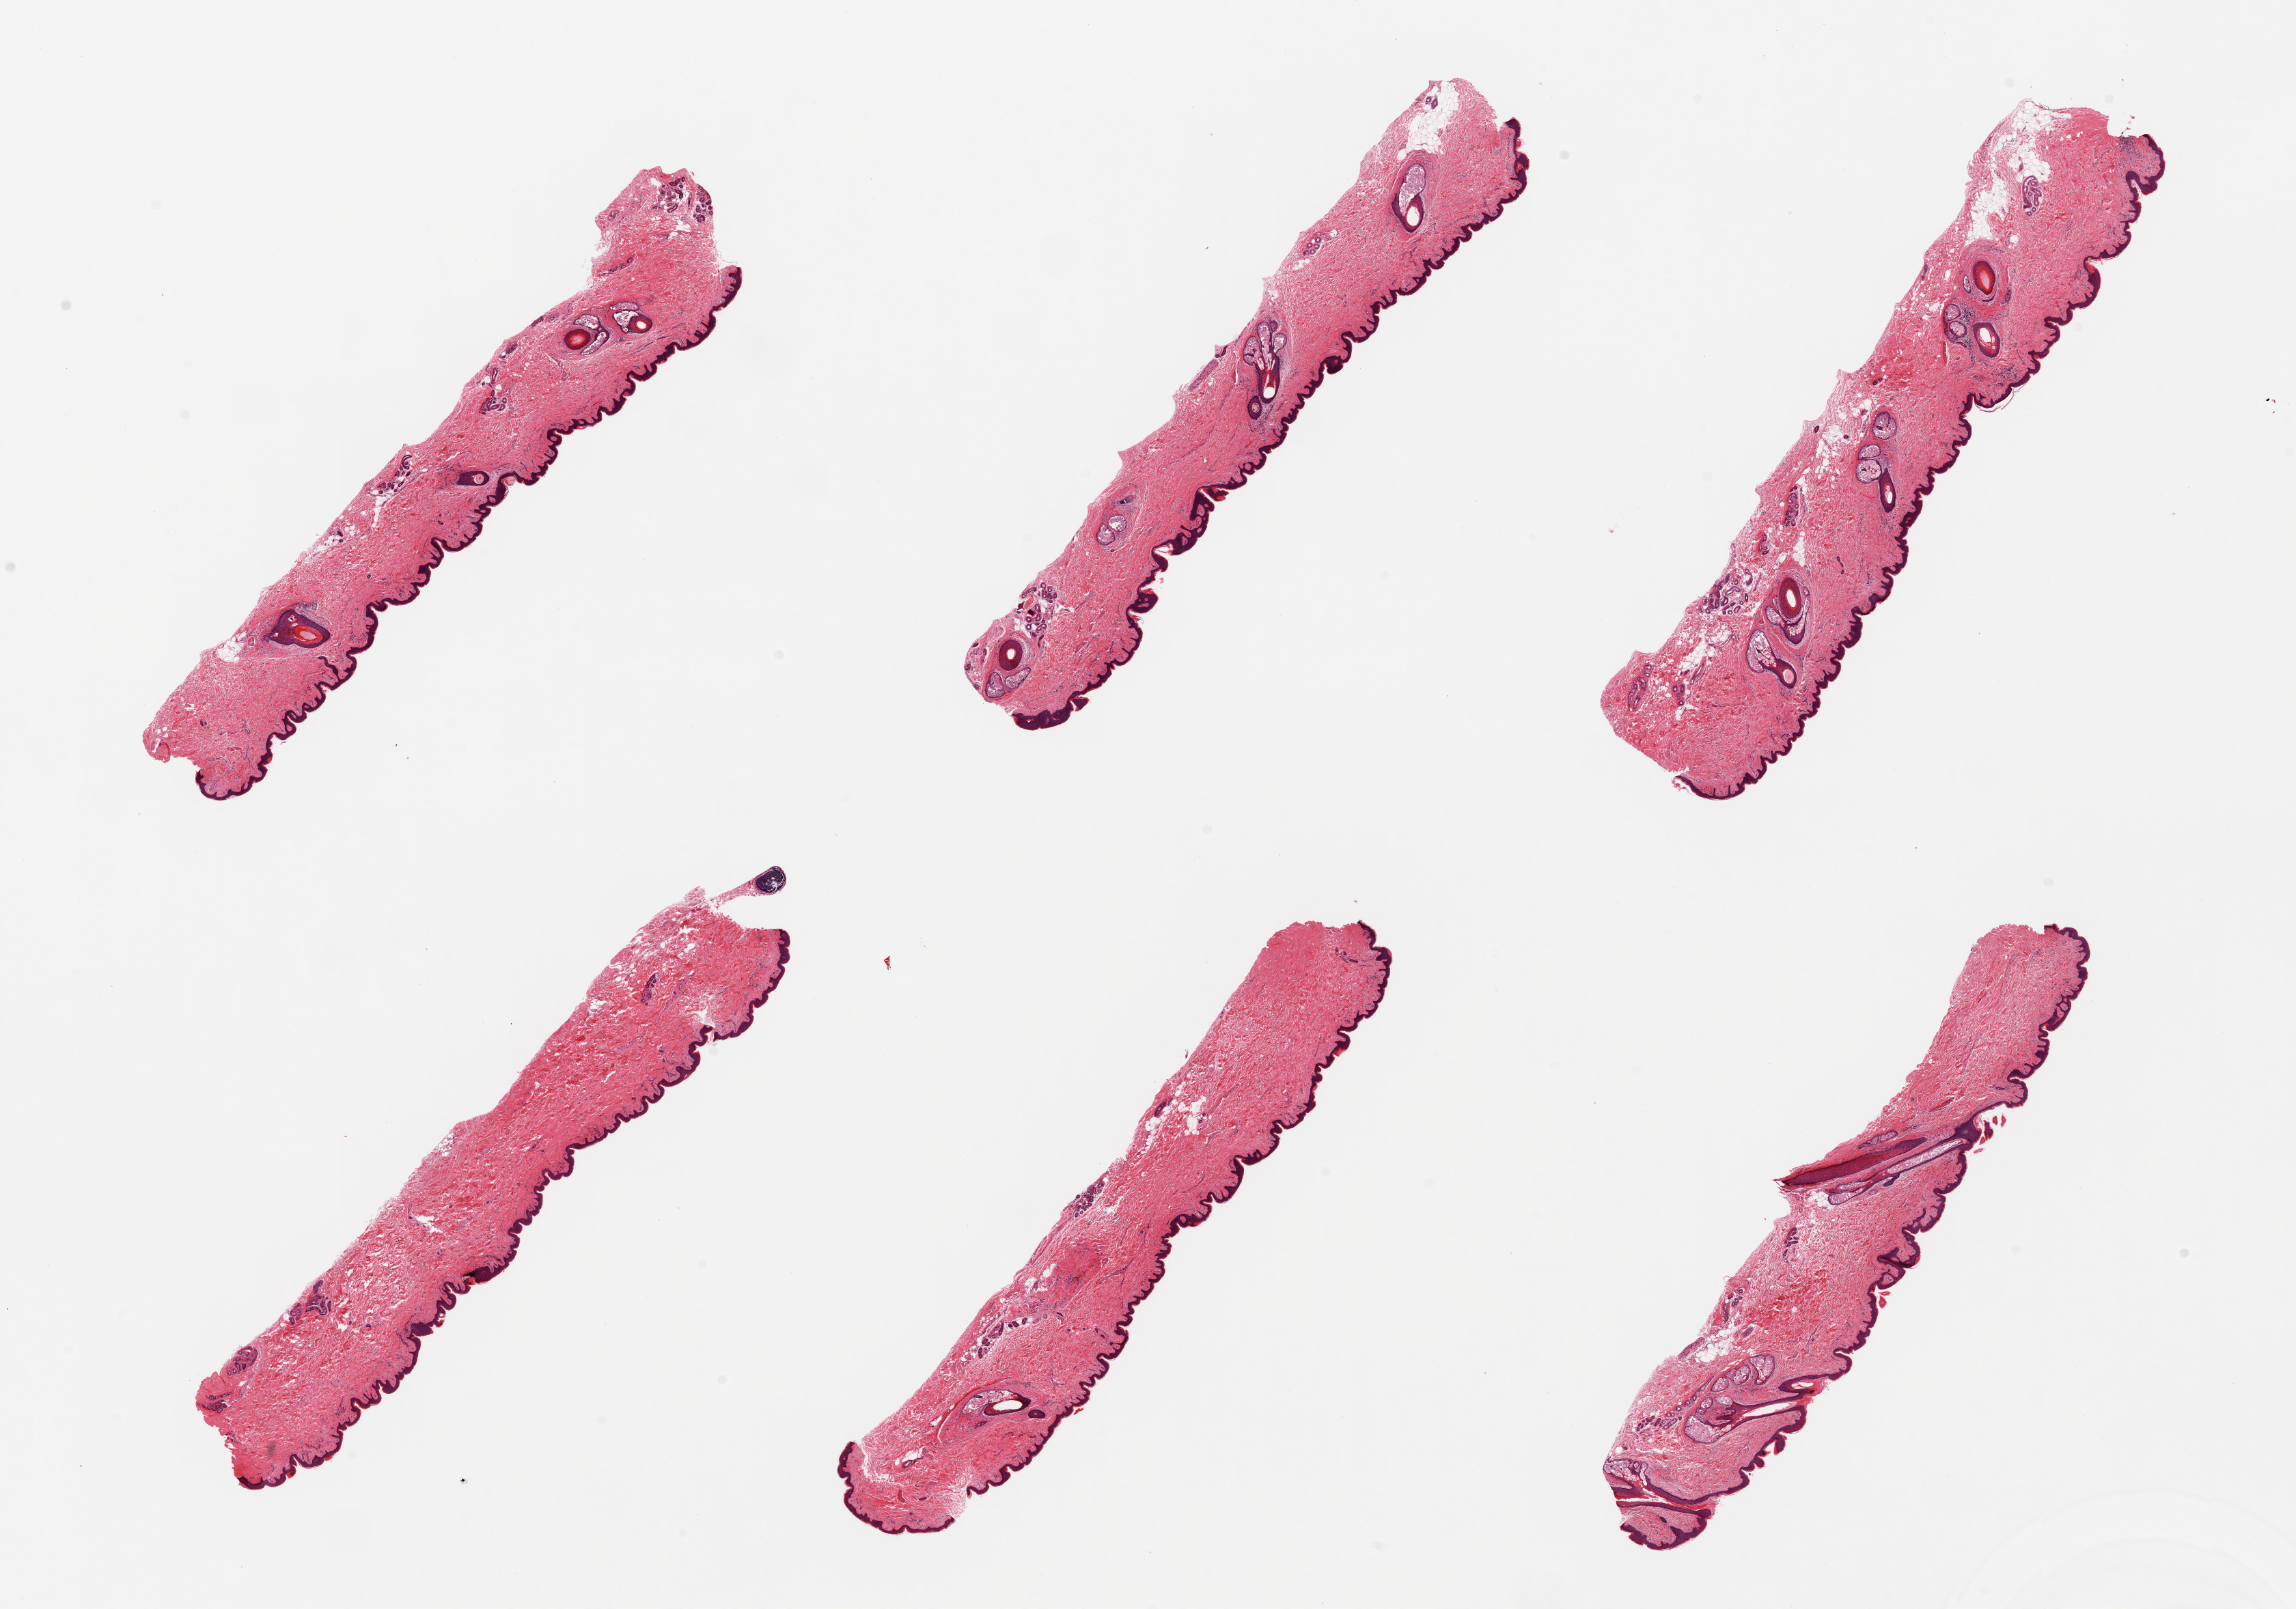
Haematoxylin and eosin whole-slide image — shown as a low-resolution overview of the whole scanned area (about 26.6 x 18.6 mm). PAXgene-fixed paraffin-embedded (PFPE) section. Section of skin of suprapubic region (target tissue). Donor tissue sample. Male donor.
Reviewer comment on this tissue sample: 6 pieces; hair-bearing skin with small amount of internal fat.